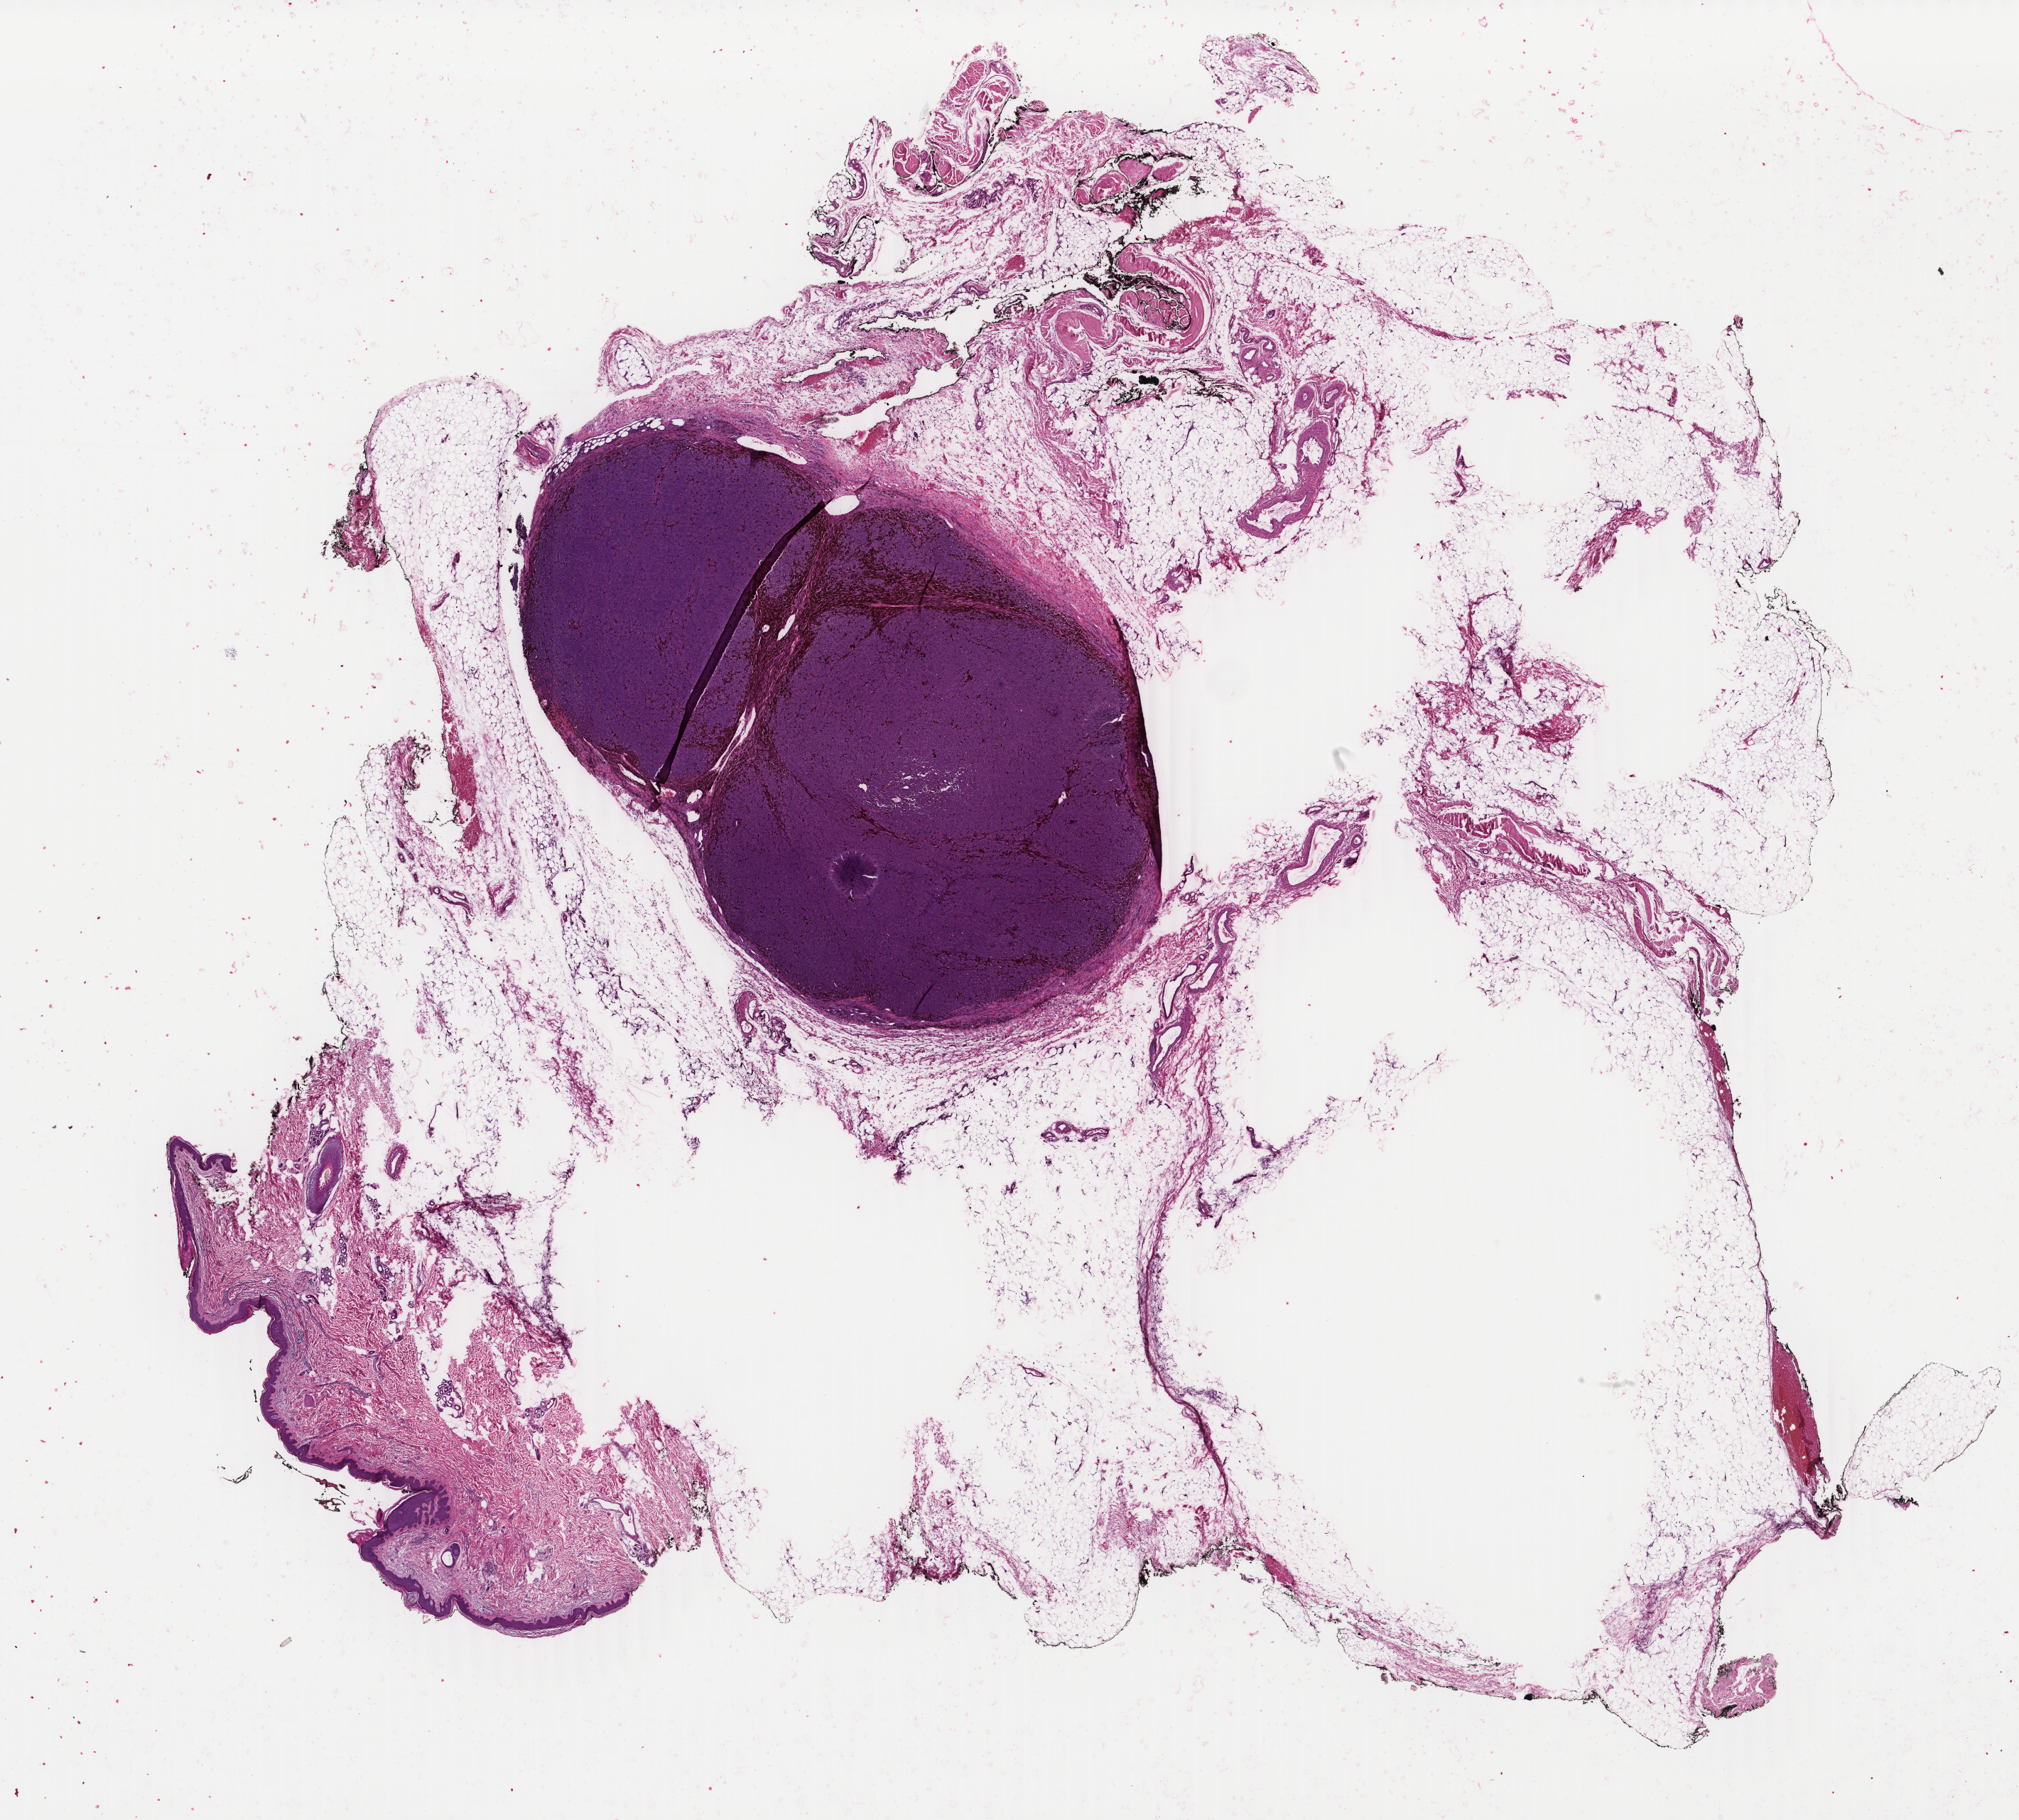
H&E whole-slide image — low-resolution overview of the scanned area, about 22.6 x 20.4 mm (from a 40x scan), formalin-fixed paraffin-embedded (FFPE) diagnostic section, sample: primary tumour, skin. Male patient; age at initial diagnosis 67 years.
Pathologic diagnosis: Malignant melanoma, NOS.